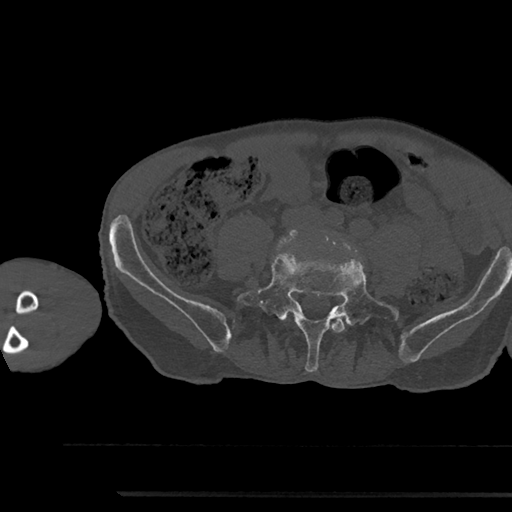
CT including the spine, one axial slice; slice 360 of 797 in the series (ordered by position); 120 kVp; bone window (W 1800 / L 400 HU); 0.5 mm slice thickness; 512 × 512 image matrix, field of view 367 × 367 mm. Male patient, age 79 years. Case-level facts recorded for this patient, not image findings: primary cancer: prostate.
Structures marked on this image (semi-automatic segmentation, software-assisted and operator-edited):
- L4 vertebra: bounding box <332,319,345,333> (left, top, right, bottom; pixels)
- L5 vertebra: <237,253,400,372>